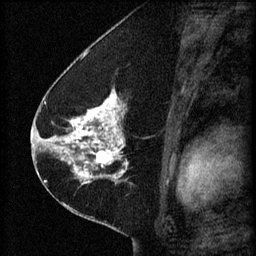
Breast MRI (dynamic contrast-enhanced), one sagittal slice; position 31 of 60 along the scan axis; 3 images stored at this slice position (order not interpretable as contrast timing); 1.5 T; TE 4.2 ms, TR 8.2 ms; 2 mm slice thickness; 256 × 256 image matrix, field of view 180 × 180 mm. Female patient, age 41 years.
Outlined on this slice (semi-automatically segmented with operator editing):
- analysis volume of interest (the breast-tissue region the enhancement analysis was run in; not a lesion): bounding box (x1, y1, x2, y2) in pixels: (67, 92, 165, 173)
- tumour enhancement mask (voxels above the 70 % enhancement threshold inside the analysis volume of interest): (67, 92, 128, 173)